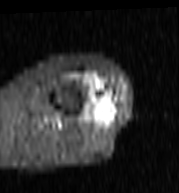
MRI of an extremity soft-tissue mass, one axial slice. Slice 27 of 103 in the series (ordered by position). STIR. MR volume resampled by the dataset authors to the PET/CT grid (not the native acquisition matrix). 3.27 mm slice thickness. 179 × 193 image matrix. Female patient. Case-level facts recorded for this patient, not image findings: histological type: undifferentiated – high grade; grade: high; site of the primary tumour: left thigh.
Structures marked on this image (expert contour drawn on MRI and transferred to this co-registered scan by the dataset authors):
- gross tumour volume including surrounding oedema: bounding box (x1, y1, x2, y2) in pixels: (75, 73, 112, 116)